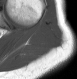
MRI of an extremity soft-tissue mass, one axial slice. Position 22 of 28 along the scan axis. MR volume resampled by the dataset authors to the PET/CT grid (not the native acquisition matrix). 3.27 mm slice thickness. 77 × 79 image matrix, field of view 75 × 77 mm. Female patient. From the clinical record (not read from this slice): histological type: malignant fibrous histiocytoma; grade: low; site of the primary tumour: left arm.
Structures marked on this image (expert contour drawn on MRI and transferred to this co-registered scan by the dataset authors):
- gross tumour volume (mass): bounding box <24,50,31,55> (left, top, right, bottom; pixels)